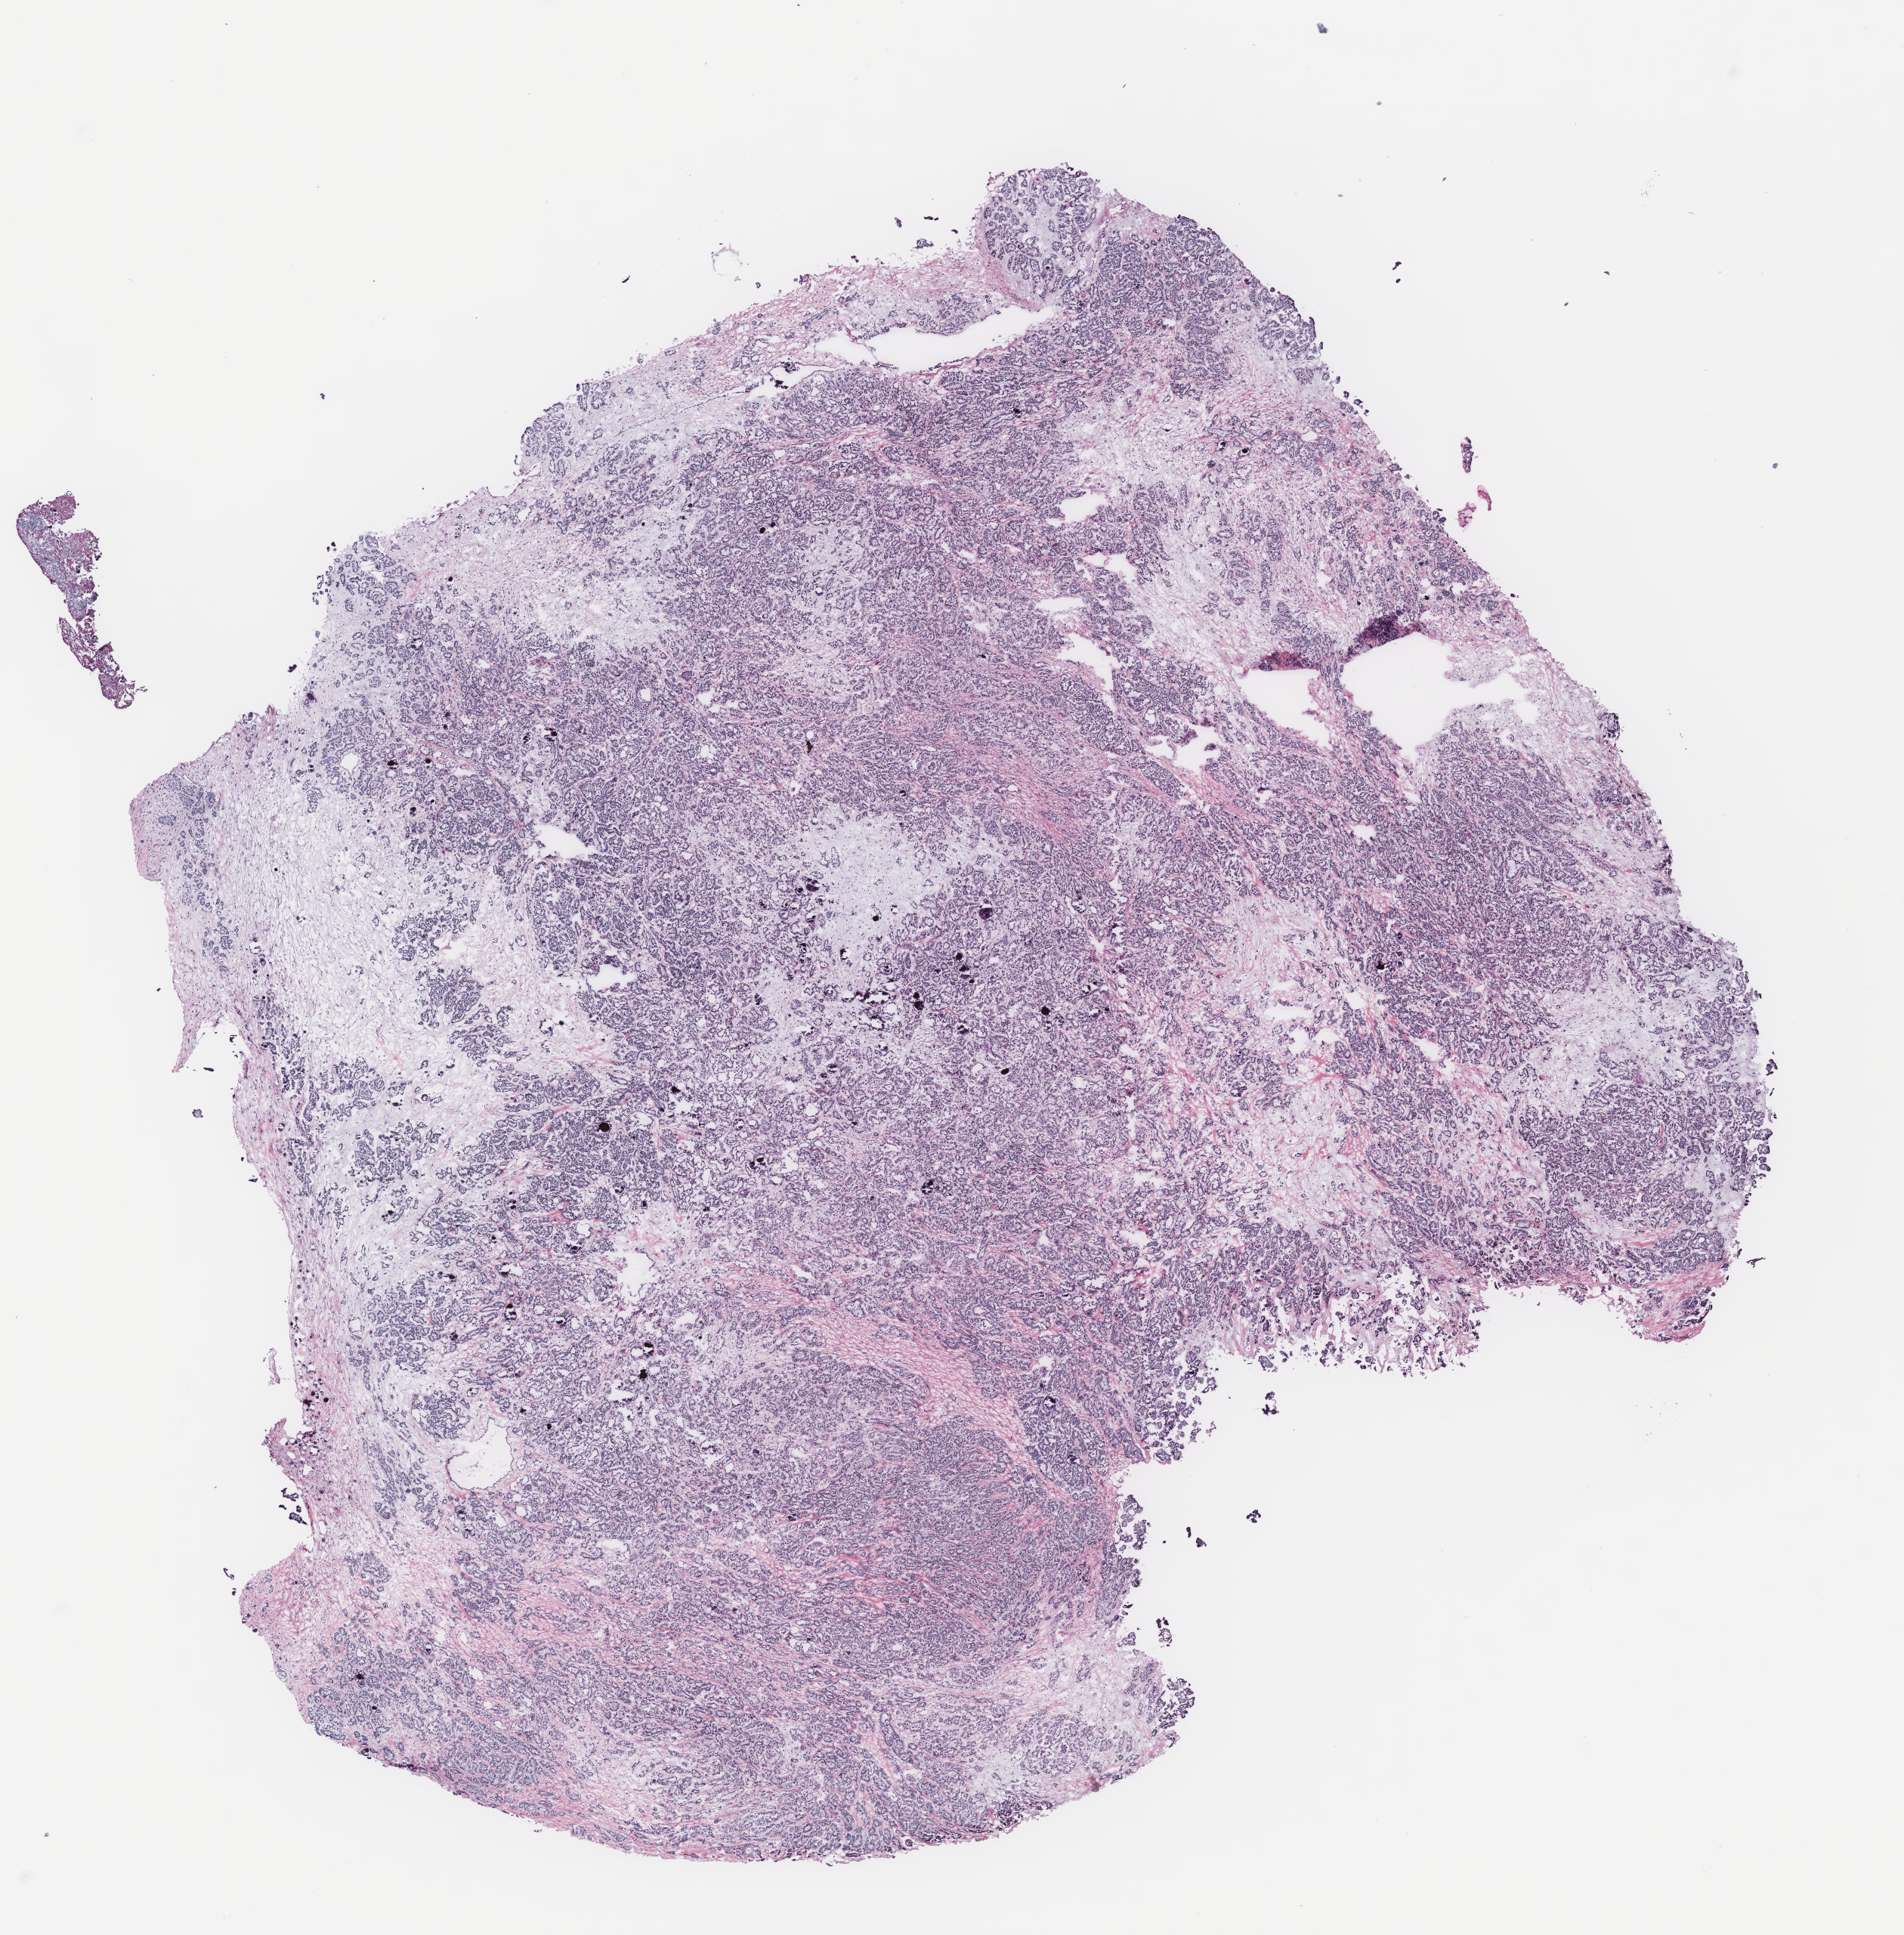
Digitized Hematoxylin and eosin (H&E) stained tissue section (whole slide) — a low-resolution overview of the entire scanned area, about 10.1 x 10.2 mm, ovary, tumour tissue. Patient: female, age 57 years.
Diagnosis: Serous adenocarcinoma, NOS. Primary tumour site (as recorded): ovary.